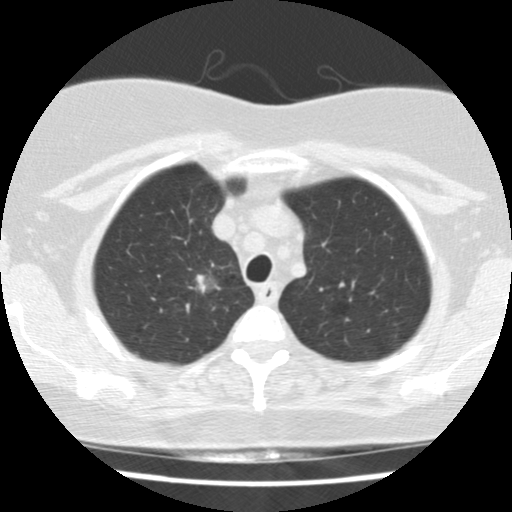
Low-dose screening chest CT, one axial slice; slice 124 of 148 in the series (ordered by position); reconstruction kernel STANDARD; lung window (W 1500 / L -600 HU); 512 × 512 image matrix, field of view 281 × 281 mm.
Outlined on this slice (expert manual segmentation):
- lesion 1 (tumor, upper lobe of right lung): bounding box (x1, y1, x2, y2) in pixels: (196, 275, 207, 292)